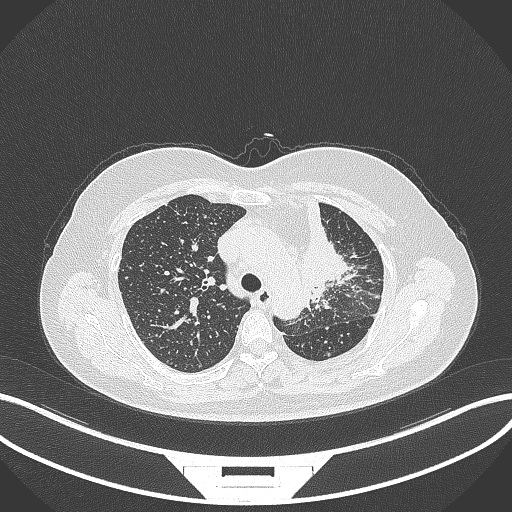
Chest CT, one axial slice; slice 241 of 348 in the series (ordered by position); reconstruction kernel B70f; 120 kVp; lung window (W 1500 / L -600 HU); 512 × 512 image matrix. Female patient, age 49 years. Case-level facts recorded for this patient, not image findings: clinical TNM (as recorded): T1c N0 M1.
Annotated regions visible in this slice (bounding box drawn by a radiologist):
- lung tumour (recorded histology: adenocarcinoma): box from (x=293, y=202) to (x=356, y=294) px